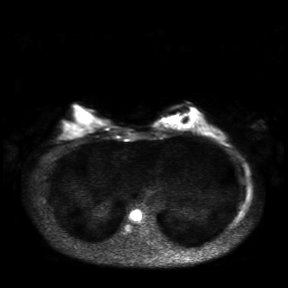
Breast MRI, one axial slice; slice 11 of 30 in the series (ordered by position); diffusion-weighted series; image 2 of 4 stored at this slice position (different b-values; order by instance number); 3 T; 4 mm slice thickness; 288 × 288 image matrix. Female patient.
Structures marked on this image (manually delineated by an expert):
- tumour on diffusion-weighted imaging: bounding box <168,117,175,125> (left, top, right, bottom; pixels)